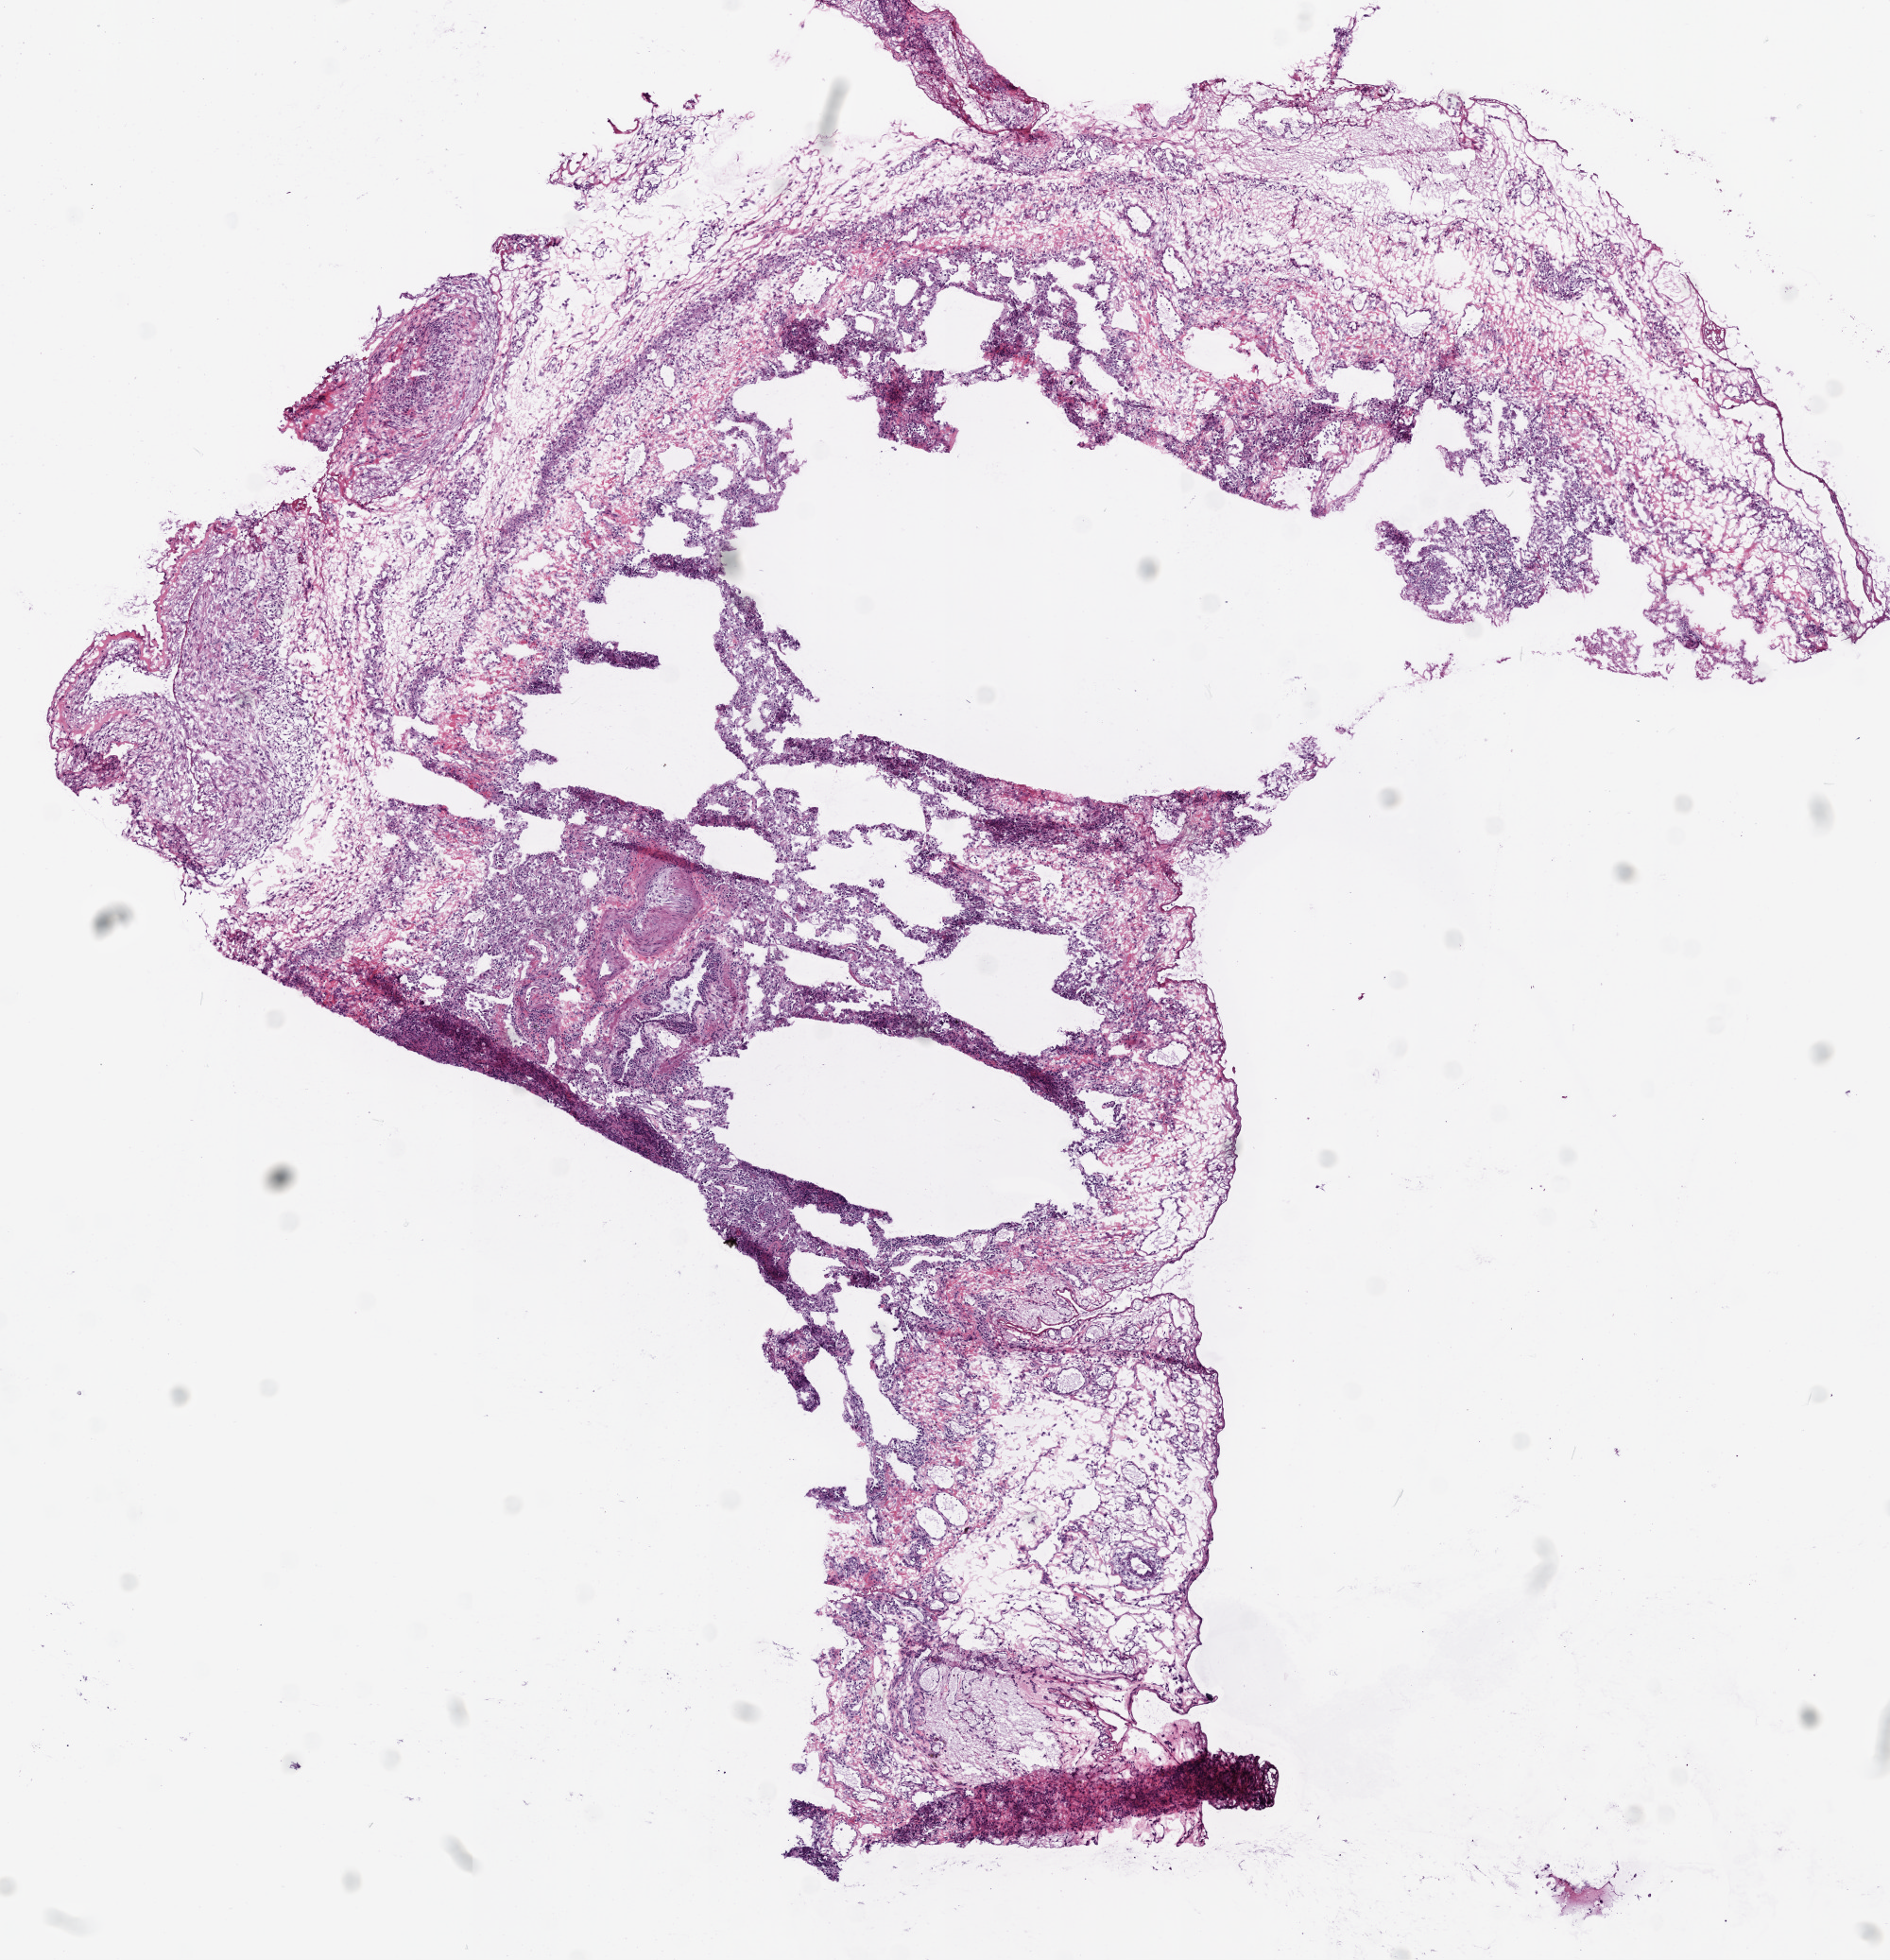
H&E-stained whole-slide image, a low-resolution overview of the entire scanned area, about 8.0 x 8.3 mm (acquisition: 20x scan); frozen section from the bottom of the tissue portion; solid tissue normal (non-tumour tissue) sample from the lung. Male, age 68 years at initial diagnosis.
This section: solid tissue normal (non-tumour) sample from the same patient. Patient diagnosis: Squamous cell carcinoma, NOS (middle lobe, lung).